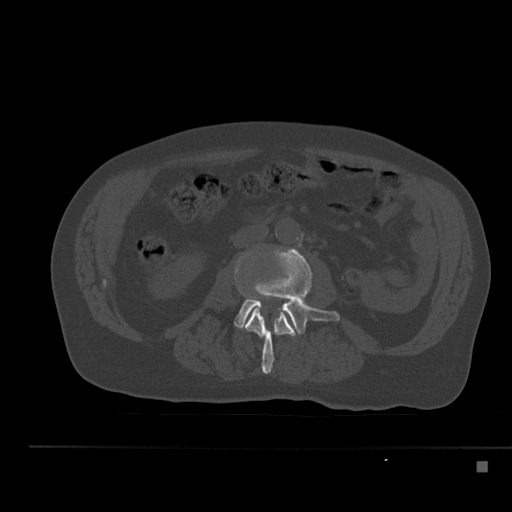
CT including the spine, one axial slice. Position 173 of 517 along the scan axis. Reconstruction kernel Br40s. Bone window (W 1800 / L 400 HU). 512 × 512 image matrix, field of view 408 × 408 mm. Patient: male, 70 years. Case-level facts recorded for this patient, not image findings: primary cancer: renal.
Annotated regions visible in this slice (semi-automatic segmentation, software-assisted and operator-edited):
- L2 vertebra: box from (x=235, y=268) to (x=296, y=374) px
- L3 vertebra: (x=234, y=249)–(x=340, y=335)